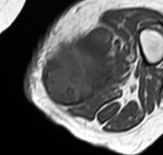
MRI of an extremity soft-tissue mass, one axial slice; slice 21 of 65 in the series (ordered by position); MR volume resampled by the dataset authors to the PET/CT grid (not the native acquisition matrix); 163 × 155 image matrix. Female patient. Case-level facts recorded for this patient, not image findings: histological type: pleomorphic leiomyosarcoma; grade: high; site of the primary tumour: left thigh.
Outlined on this slice (expert contour drawn on MRI and transferred to this co-registered scan by the dataset authors):
- gross tumour volume including surrounding oedema: bounding box <44,28,127,107> (left, top, right, bottom; pixels)
- gross tumour volume (mass): <44,47,113,107>